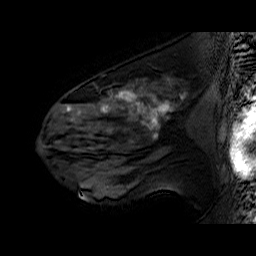
Breast MRI (dynamic contrast-enhanced), one sagittal slice. Slice 35 of 60 in the series (ordered by position). Dynamic contrast-enhanced series, time point 2 of 6 at this slice position (early post-contrast). 1.5 T. TE 6.4 ms, TR 32.9 ms. 256 × 256 image matrix. Female patient. From the clinical record (not read from this slice): setting: breast cancer imaged before/during neoadjuvant chemotherapy; receptor status: HER2-positive.
Structures marked on this image (semi-automatic segmentation, software-assisted and operator-edited):
- analysis volume of interest (the breast-tissue region the enhancement analysis was run in; not a lesion): bounding box [x1, y1, x2, y2] px = [51, 78, 196, 160]
- tumour enhancement mask (voxels above the 100 % enhancement threshold inside the analysis volume of interest): [67, 90, 173, 137]